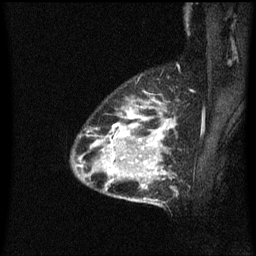
Breast MRI (dynamic contrast-enhanced), one sagittal slice; slice 47 of 60 in the series (ordered by position); dynamic contrast-enhanced series, image 2 of 3 at this slice position (ordered by acquisition); 1.5 T; TE 4.2 ms, TR 8.4 ms; 2 mm slice thickness; 256 × 256 image matrix. Patient: female, 34 years. From the clinical record (not read from this slice): setting: breast cancer imaged before/during neoadjuvant chemotherapy; receptor status: HR-positive, HER2-negative.
Outlined on this slice (semi-automatically segmented with operator editing):
- analysis volume of interest (the breast-tissue region the enhancement analysis was run in; not a lesion): bounding box (x1, y1, x2, y2) in pixels: (73, 100, 176, 207)
- tumour enhancement mask (voxels above the 70 % enhancement threshold inside the analysis volume of interest): (96, 102, 175, 175)